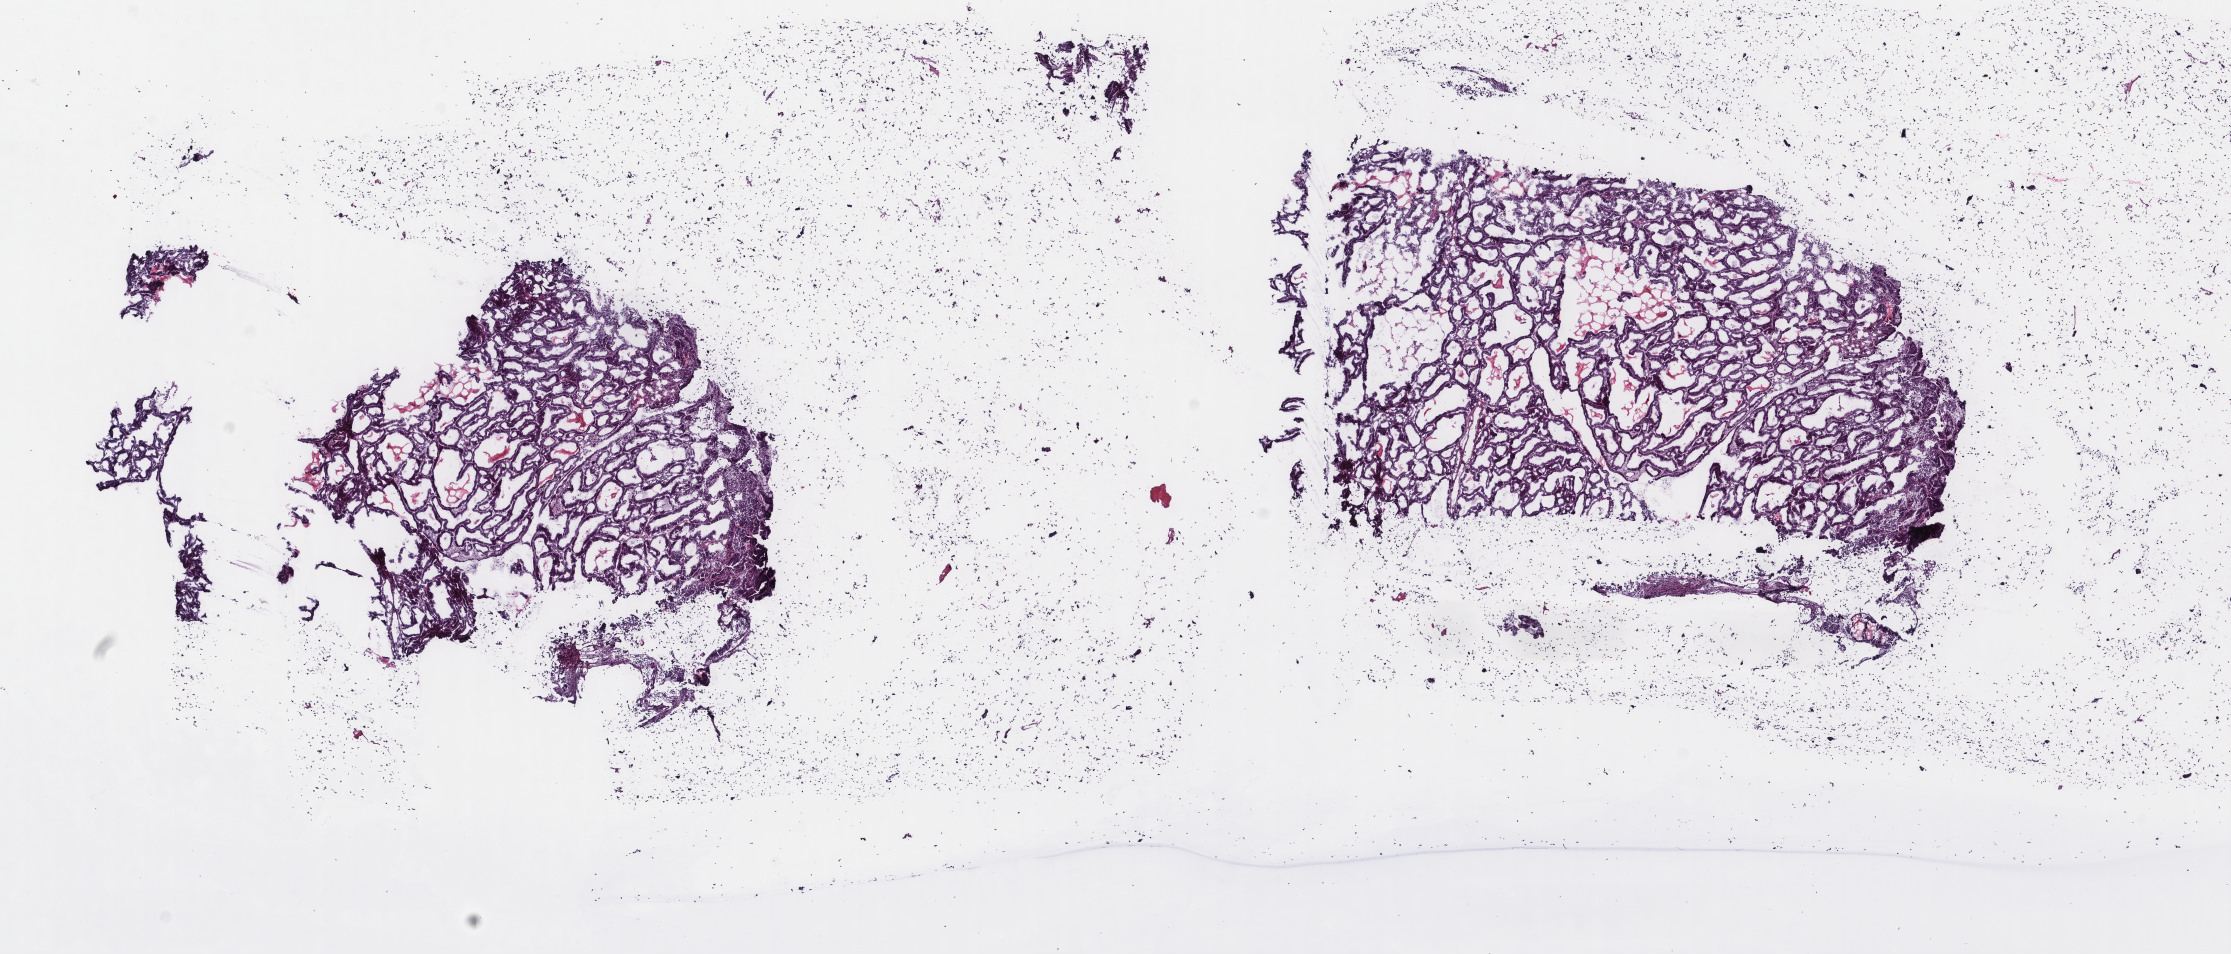
Hematoxylin and eosin (H&E) stained whole-slide image, whole scanned area (about 17.7 x 7.6 mm, slide scanned at 40x) shown as a low-resolution overview; frozen section from the top of the tissue portion; uterus, primary tumour sample. Patient: female, age at initial diagnosis 59 years. Histologic grade: G1 (well differentiated). Composition of this section per pathologist review: tumour cells 100%, tumour nuclei 90%, normal cells 0%, stromal cells 0%, necrosis 0%. Infiltration values recorded for this section: lymphocyte infiltration 0%, monocyte infiltration 0%, neutrophil infiltration 0%.
* histologic diagnosis: Endometrioid adenocarcinoma, NOS (endometrium)
* FIGO stage: IA